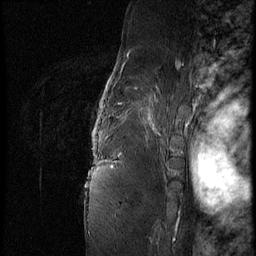
Breast MRI (dynamic contrast-enhanced), one sagittal slice. Slice 58 of 62 in the series (ordered by position). 3 images stored at this slice position (order not interpretable as contrast timing). 1.5 T. TE 4.2 ms, TR 9 ms. 256 × 256 image matrix, field of view 180 × 180 mm. Patient: female, 56 years. Case-level facts recorded for this patient, not image findings: setting: breast cancer imaged before/during neoadjuvant chemotherapy; receptor status: HER2-positive.
Structures marked on this image (semi-automatic segmentation, software-assisted and operator-edited):
- analysis volume of interest (the breast-tissue region the enhancement analysis was run in; not a lesion): bounding box [x1, y1, x2, y2] px = [85, 75, 181, 153]
- tumour enhancement mask (voxels above the 140 % enhancement threshold inside the analysis volume of interest): [102, 86, 159, 134]